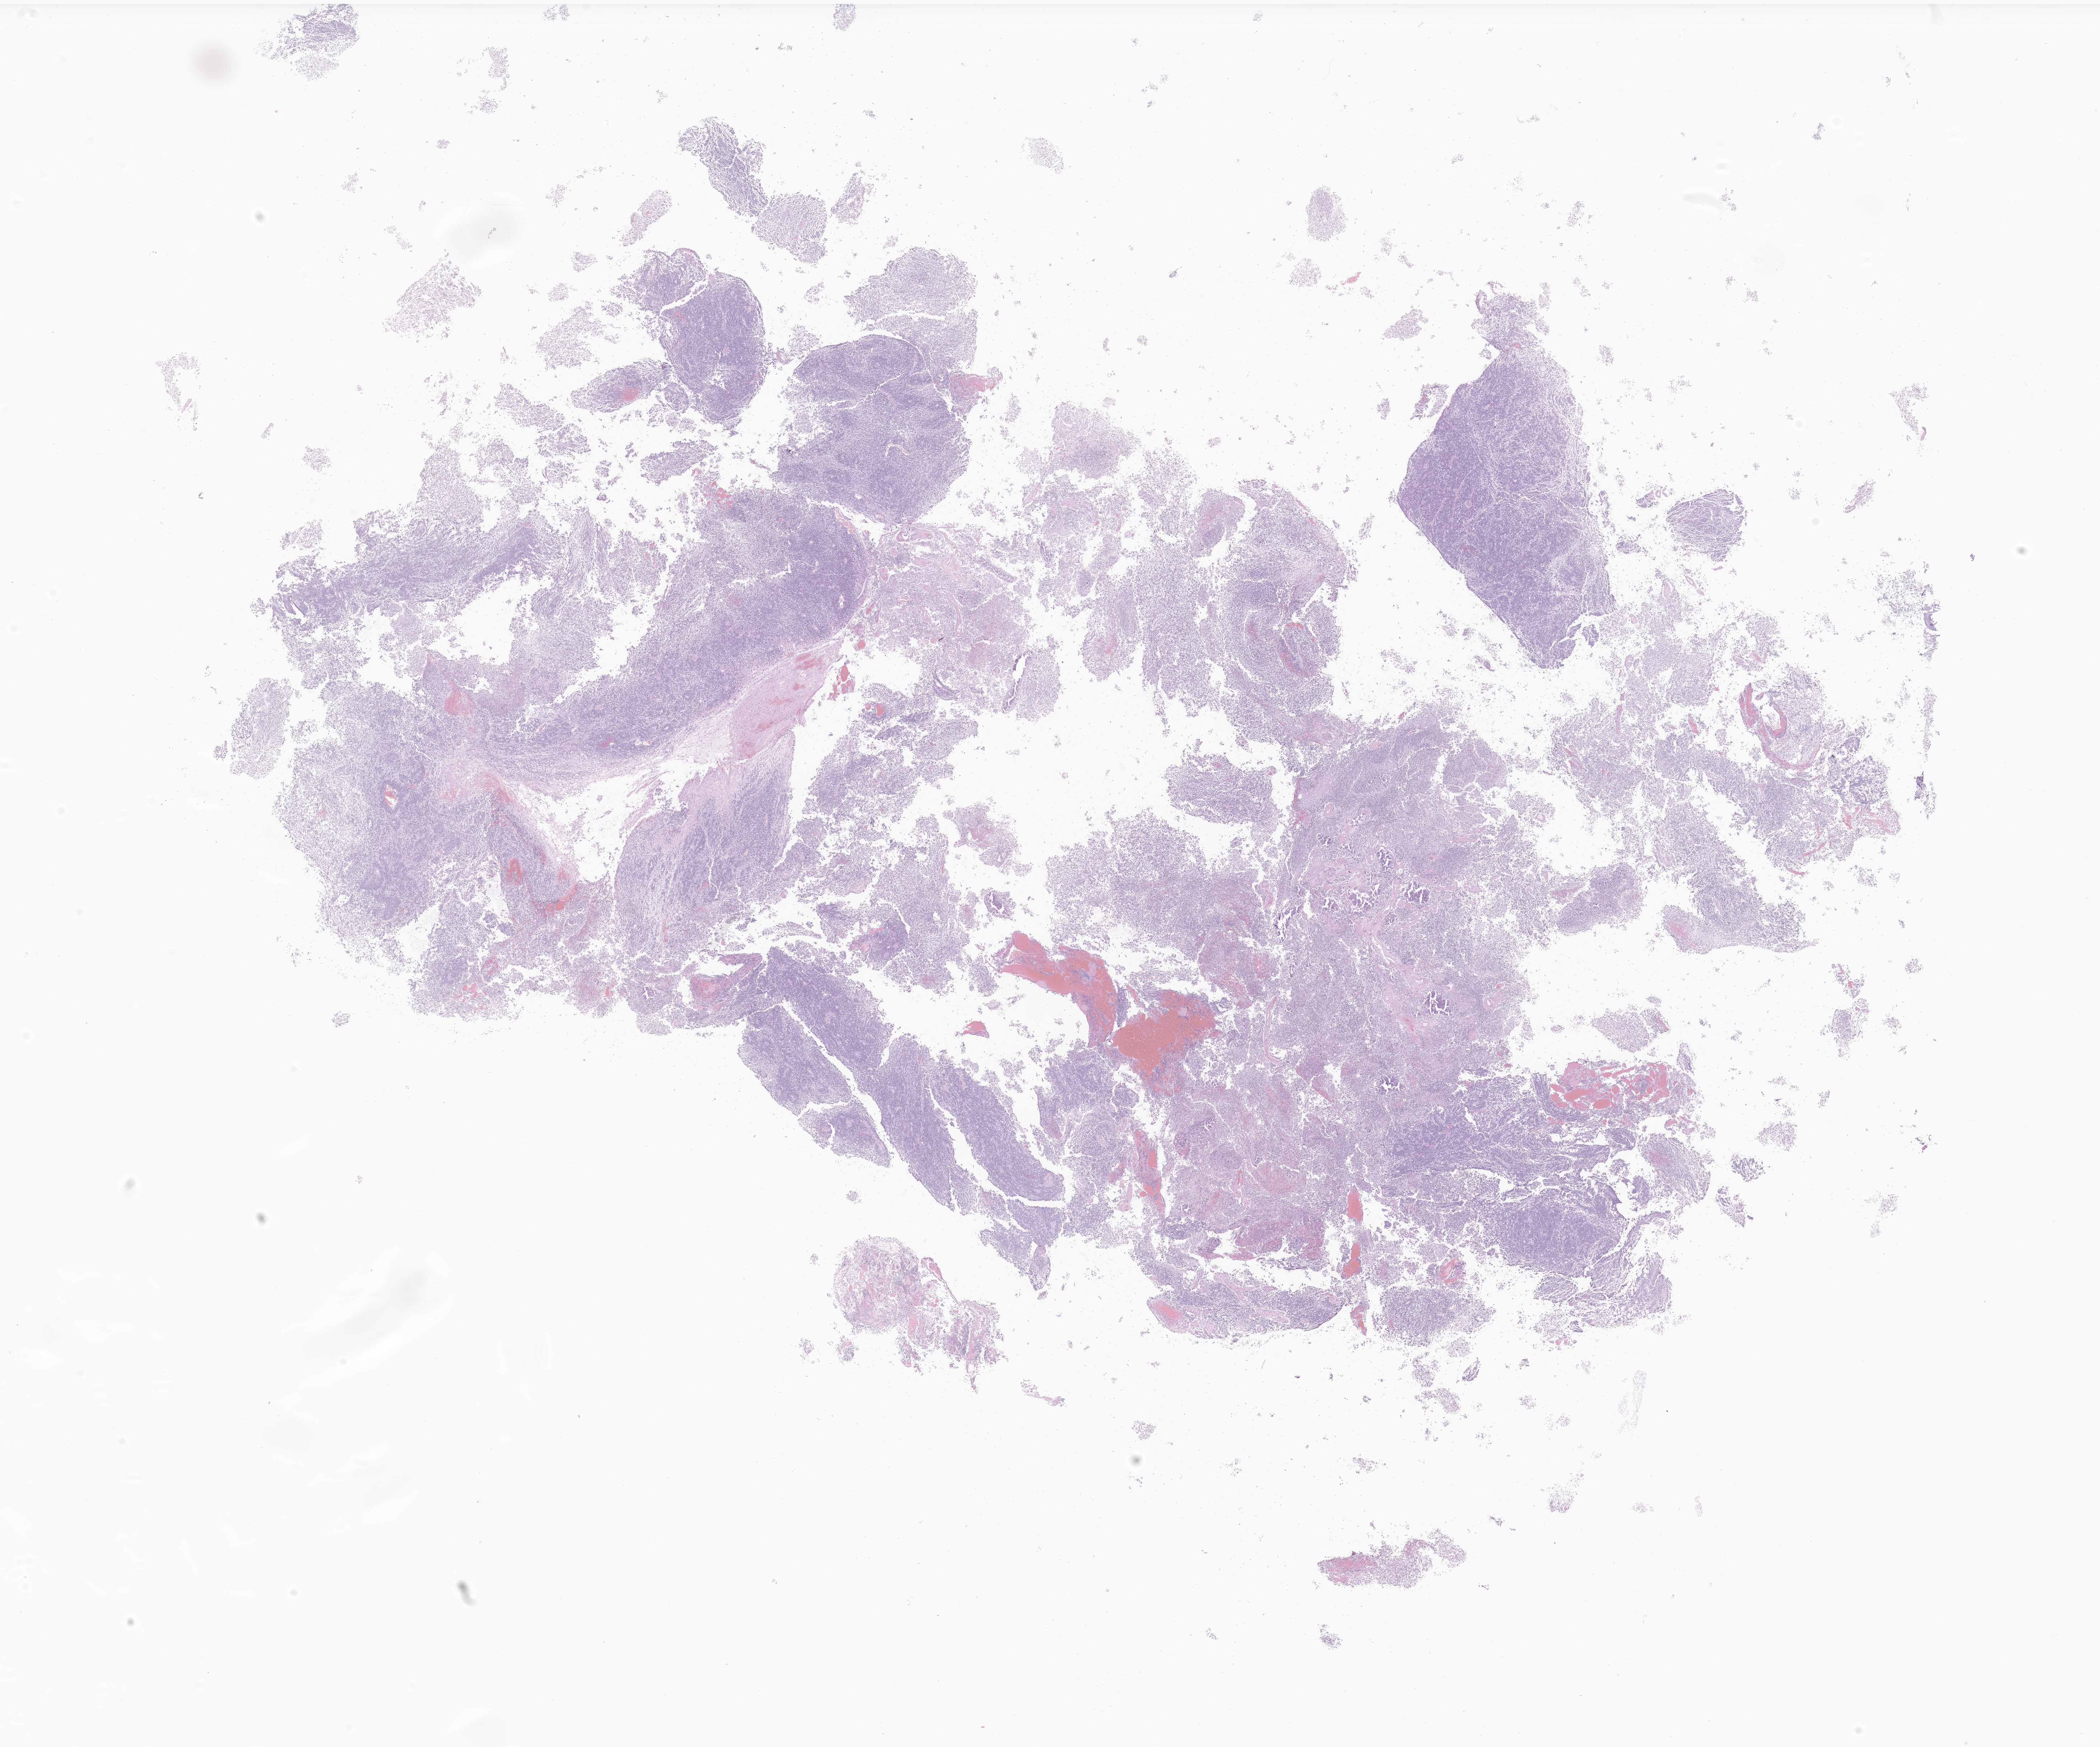
Digitized H&E-stained section of tumor tissue from the occipital lobe, shown as a low-resolution overview of the whole scanned area (about 24.7 x 20.5 mm), formalin-fixed paraffin-embedded section. Patient: male, age 218 days.
Diagnosis: Tumor cells, malignant.